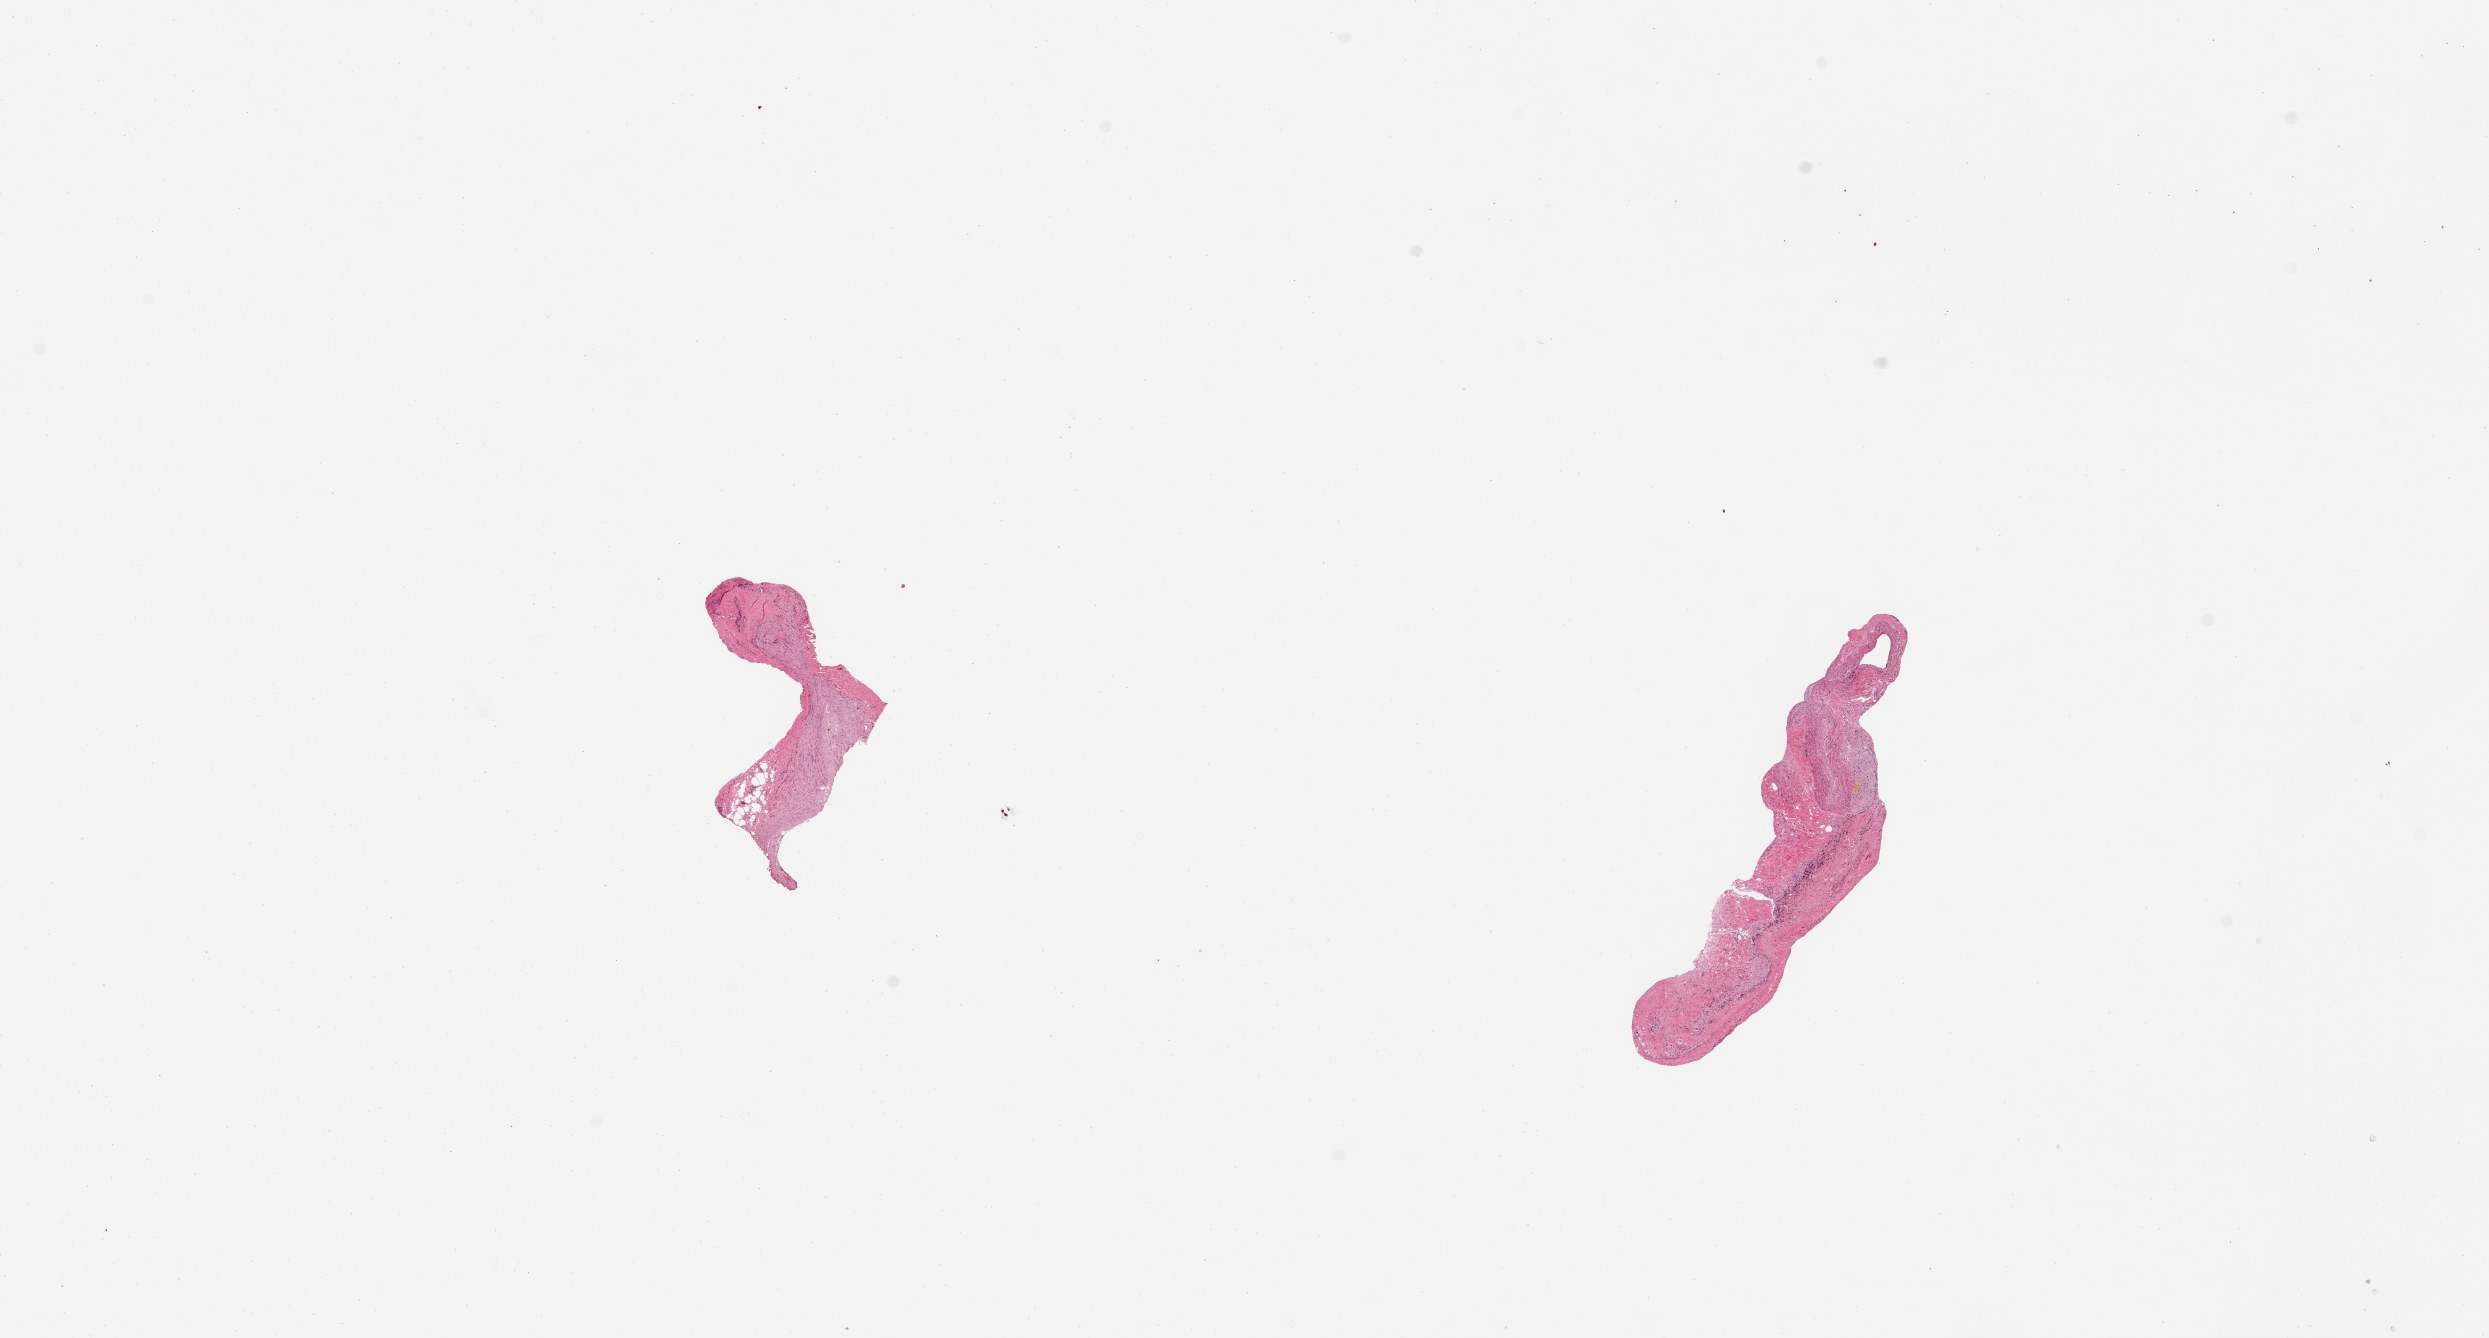
Digitized haematoxylin and eosin-stained section — a low-resolution overview of the entire scanned area, about 19.7 x 10.6 mm. Donor sex: female.
Specimen: PAXgene-fixed, paraffin-embedded tissue; sampled site (target tissue): tibial artery; tissue donor sample.